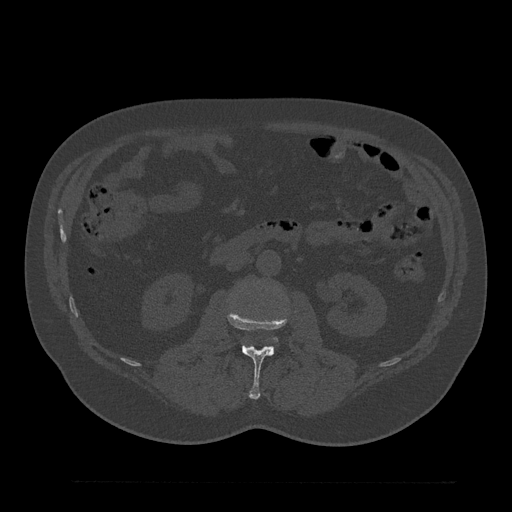
CT including the spine, one axial slice. Position 81 of 797 along the scan axis. 120 kVp. Bone window (W 1800 / L 400 HU). 0.5 mm slice thickness. 512 × 512 image matrix. Male patient, age 61 years. From the clinical record (not read from this slice): primary cancer: prostate.
Outlined on this slice (semi-automatic segmentation, software-assisted and operator-edited):
- L2 vertebra: bounding box [x1, y1, x2, y2] px = [227, 310, 288, 400]